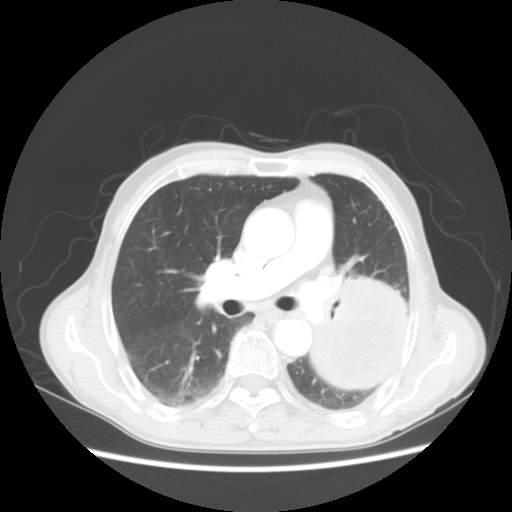
Chest CT, one axial slice; slice 30 of 51 in the series (ordered by position); reconstruction kernel STANDARD; 120 kVp; lung window (W 1500 / L -600 HU); 5 mm slice thickness; 512 × 512 image matrix, field of view 360 × 360 mm. Male patient, age 64 years. Case-level facts recorded for this patient, not image findings: clinical TNM (as recorded): T4 N0 M0.
Outlined on this slice (bounding box drawn by a radiologist):
- lung tumour (recorded histology: squamous cell carcinoma): bounding box (x1, y1, x2, y2) in pixels: (291, 270, 417, 403)